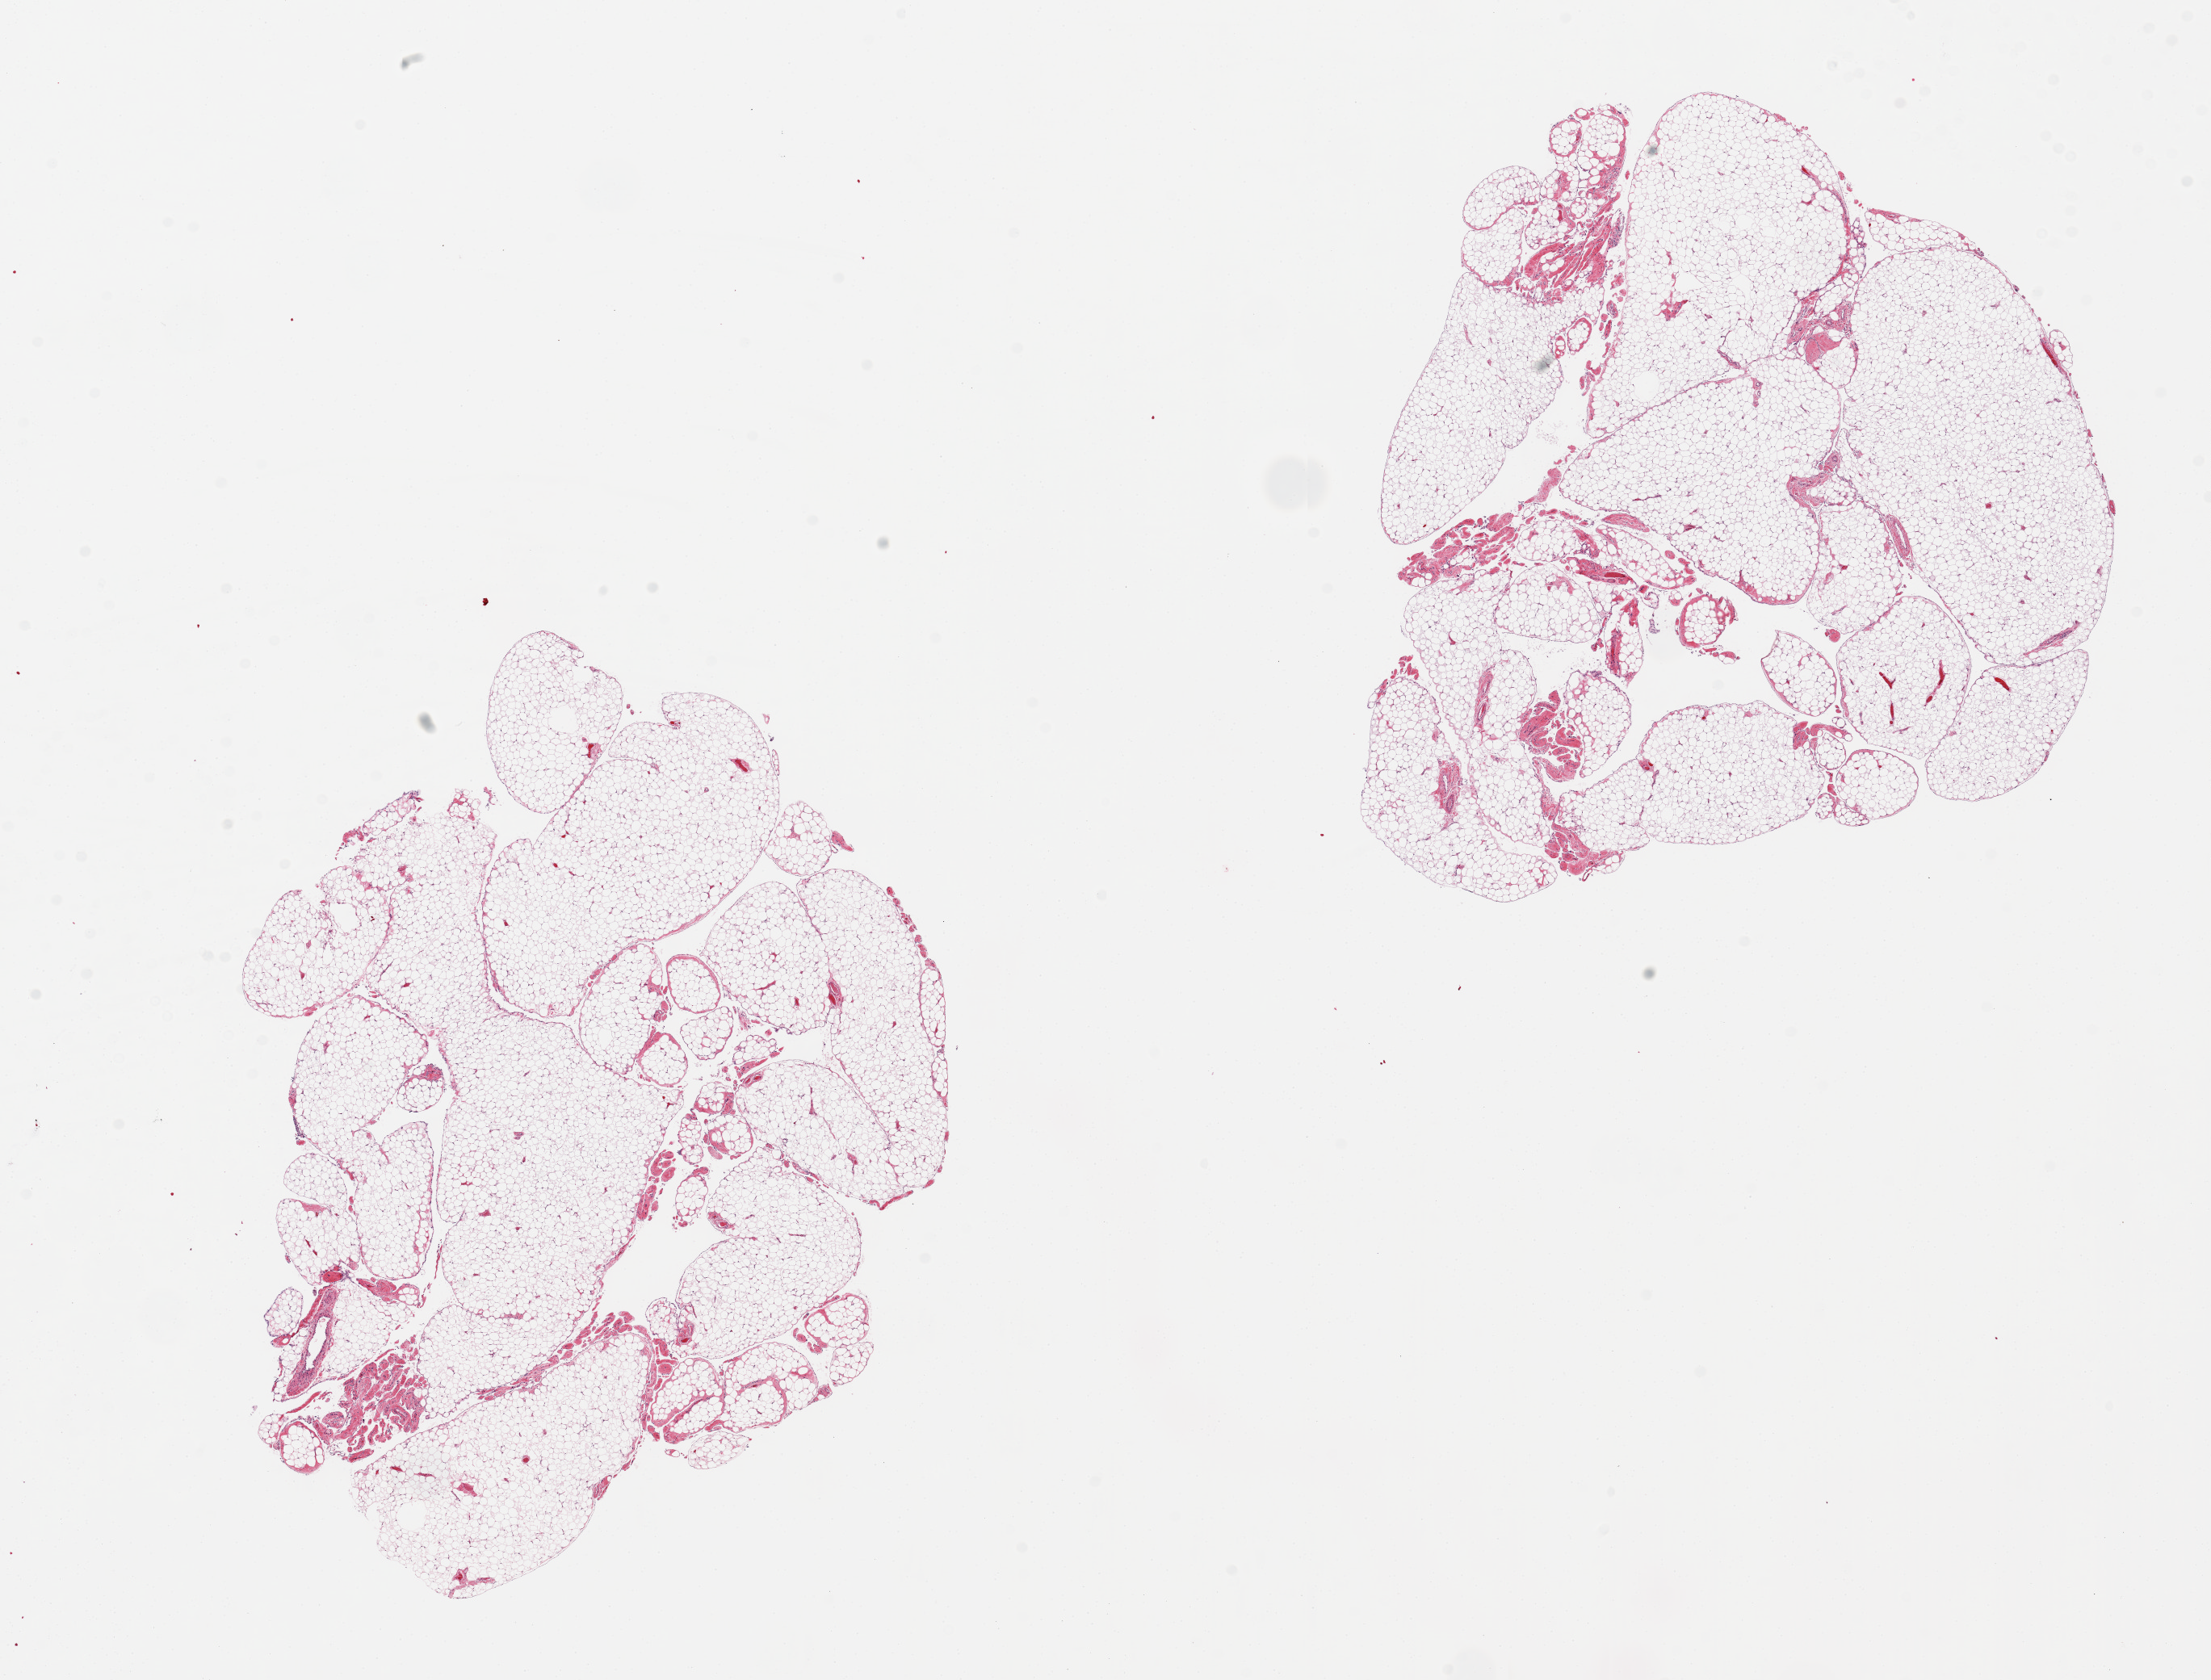
H&E whole-slide image, low-resolution overview of the scanned area, about 21.7 x 16.5 mm. PAXgene-fixed, paraffin-embedded tissue. Target tissue: omentum. Donor tissue sample.
Review note (as recorded): 2 pieces, 8x7 & 8x8mm; no artifacts.